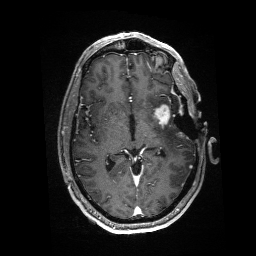
Brain MRI from a brain-tumour surgery series, one axial slice. Slice 89 of 176 in the series (ordered by position). T1-weighted post-contrast. 256 × 256 image matrix, field of view 256 × 256 mm. Case-level facts recorded for this patient, not image findings: histopathology: Glioblastoma; WHO grade: 4; IDH mutation: no.
Outlined on this slice (manually delineated by an expert):
- residual tumour: box from (x=154, y=104) to (x=181, y=125) px